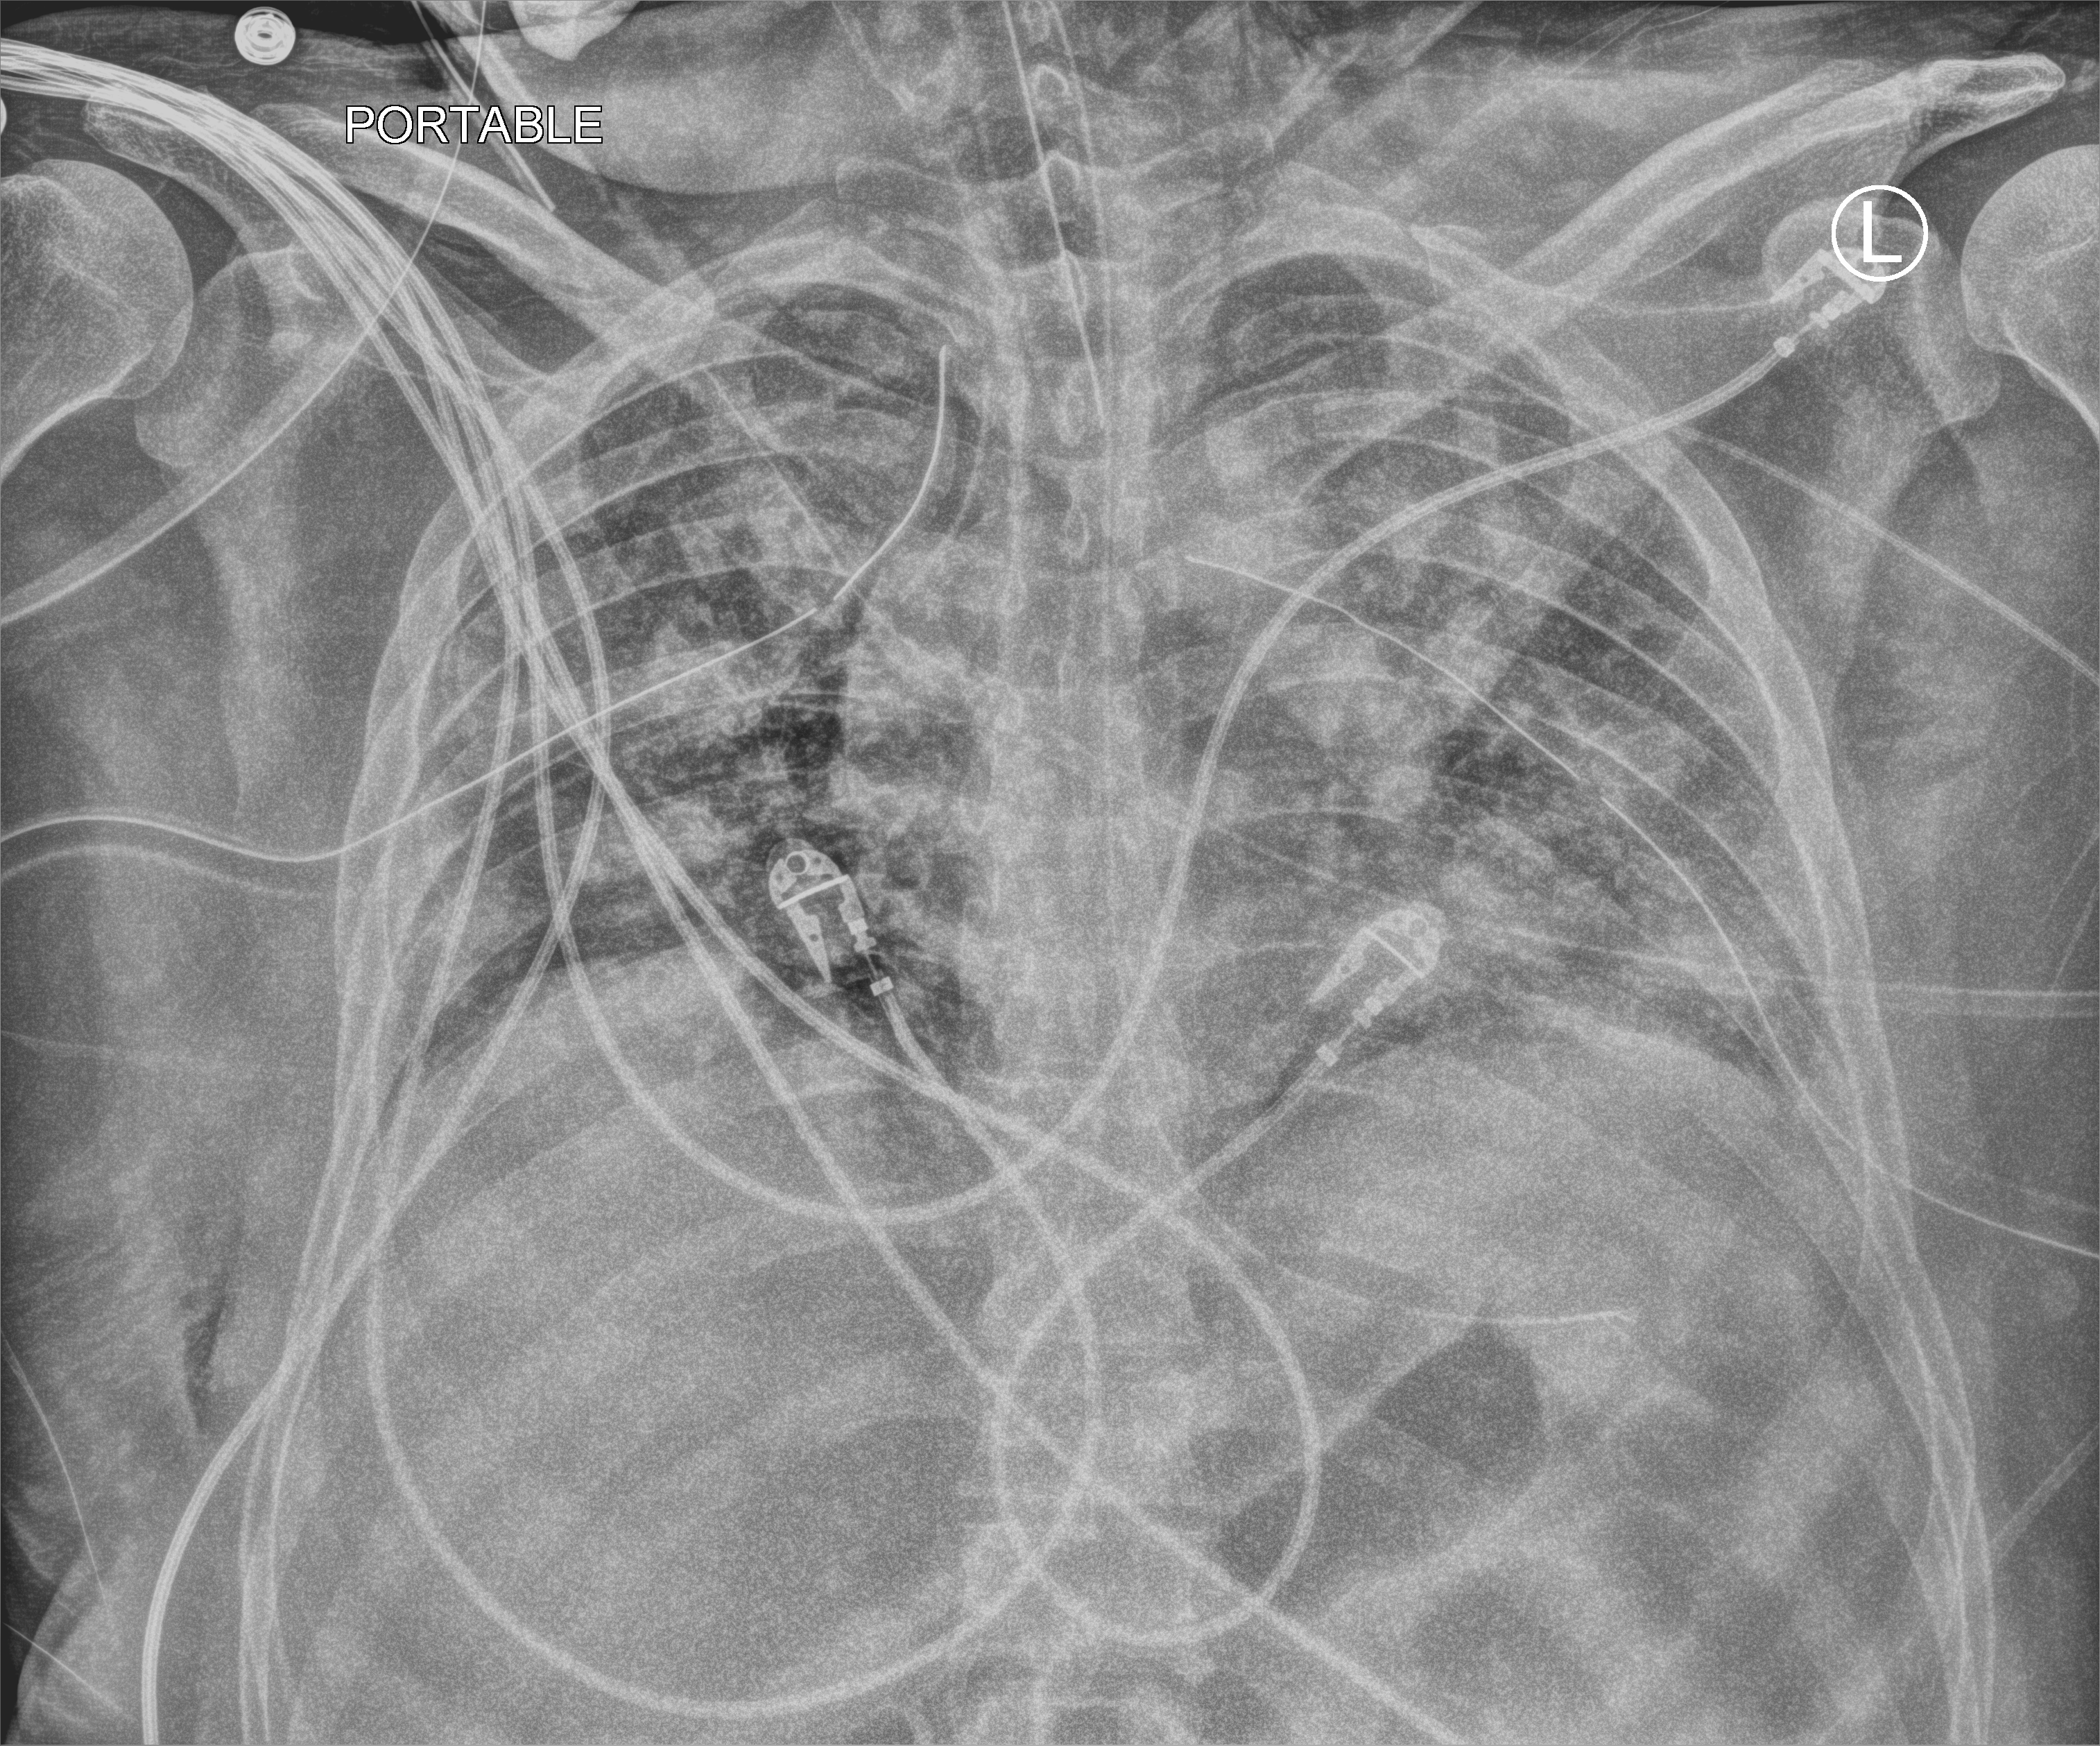
Portable chest radiograph, anteroposterior (AP) projection. Male patient hospitalised with COVID-19, age 18–59 years.
Admission-level facts for this patient (not findings on this image; timing relative to this image not recorded): chronic kidney disease (admission record): no.